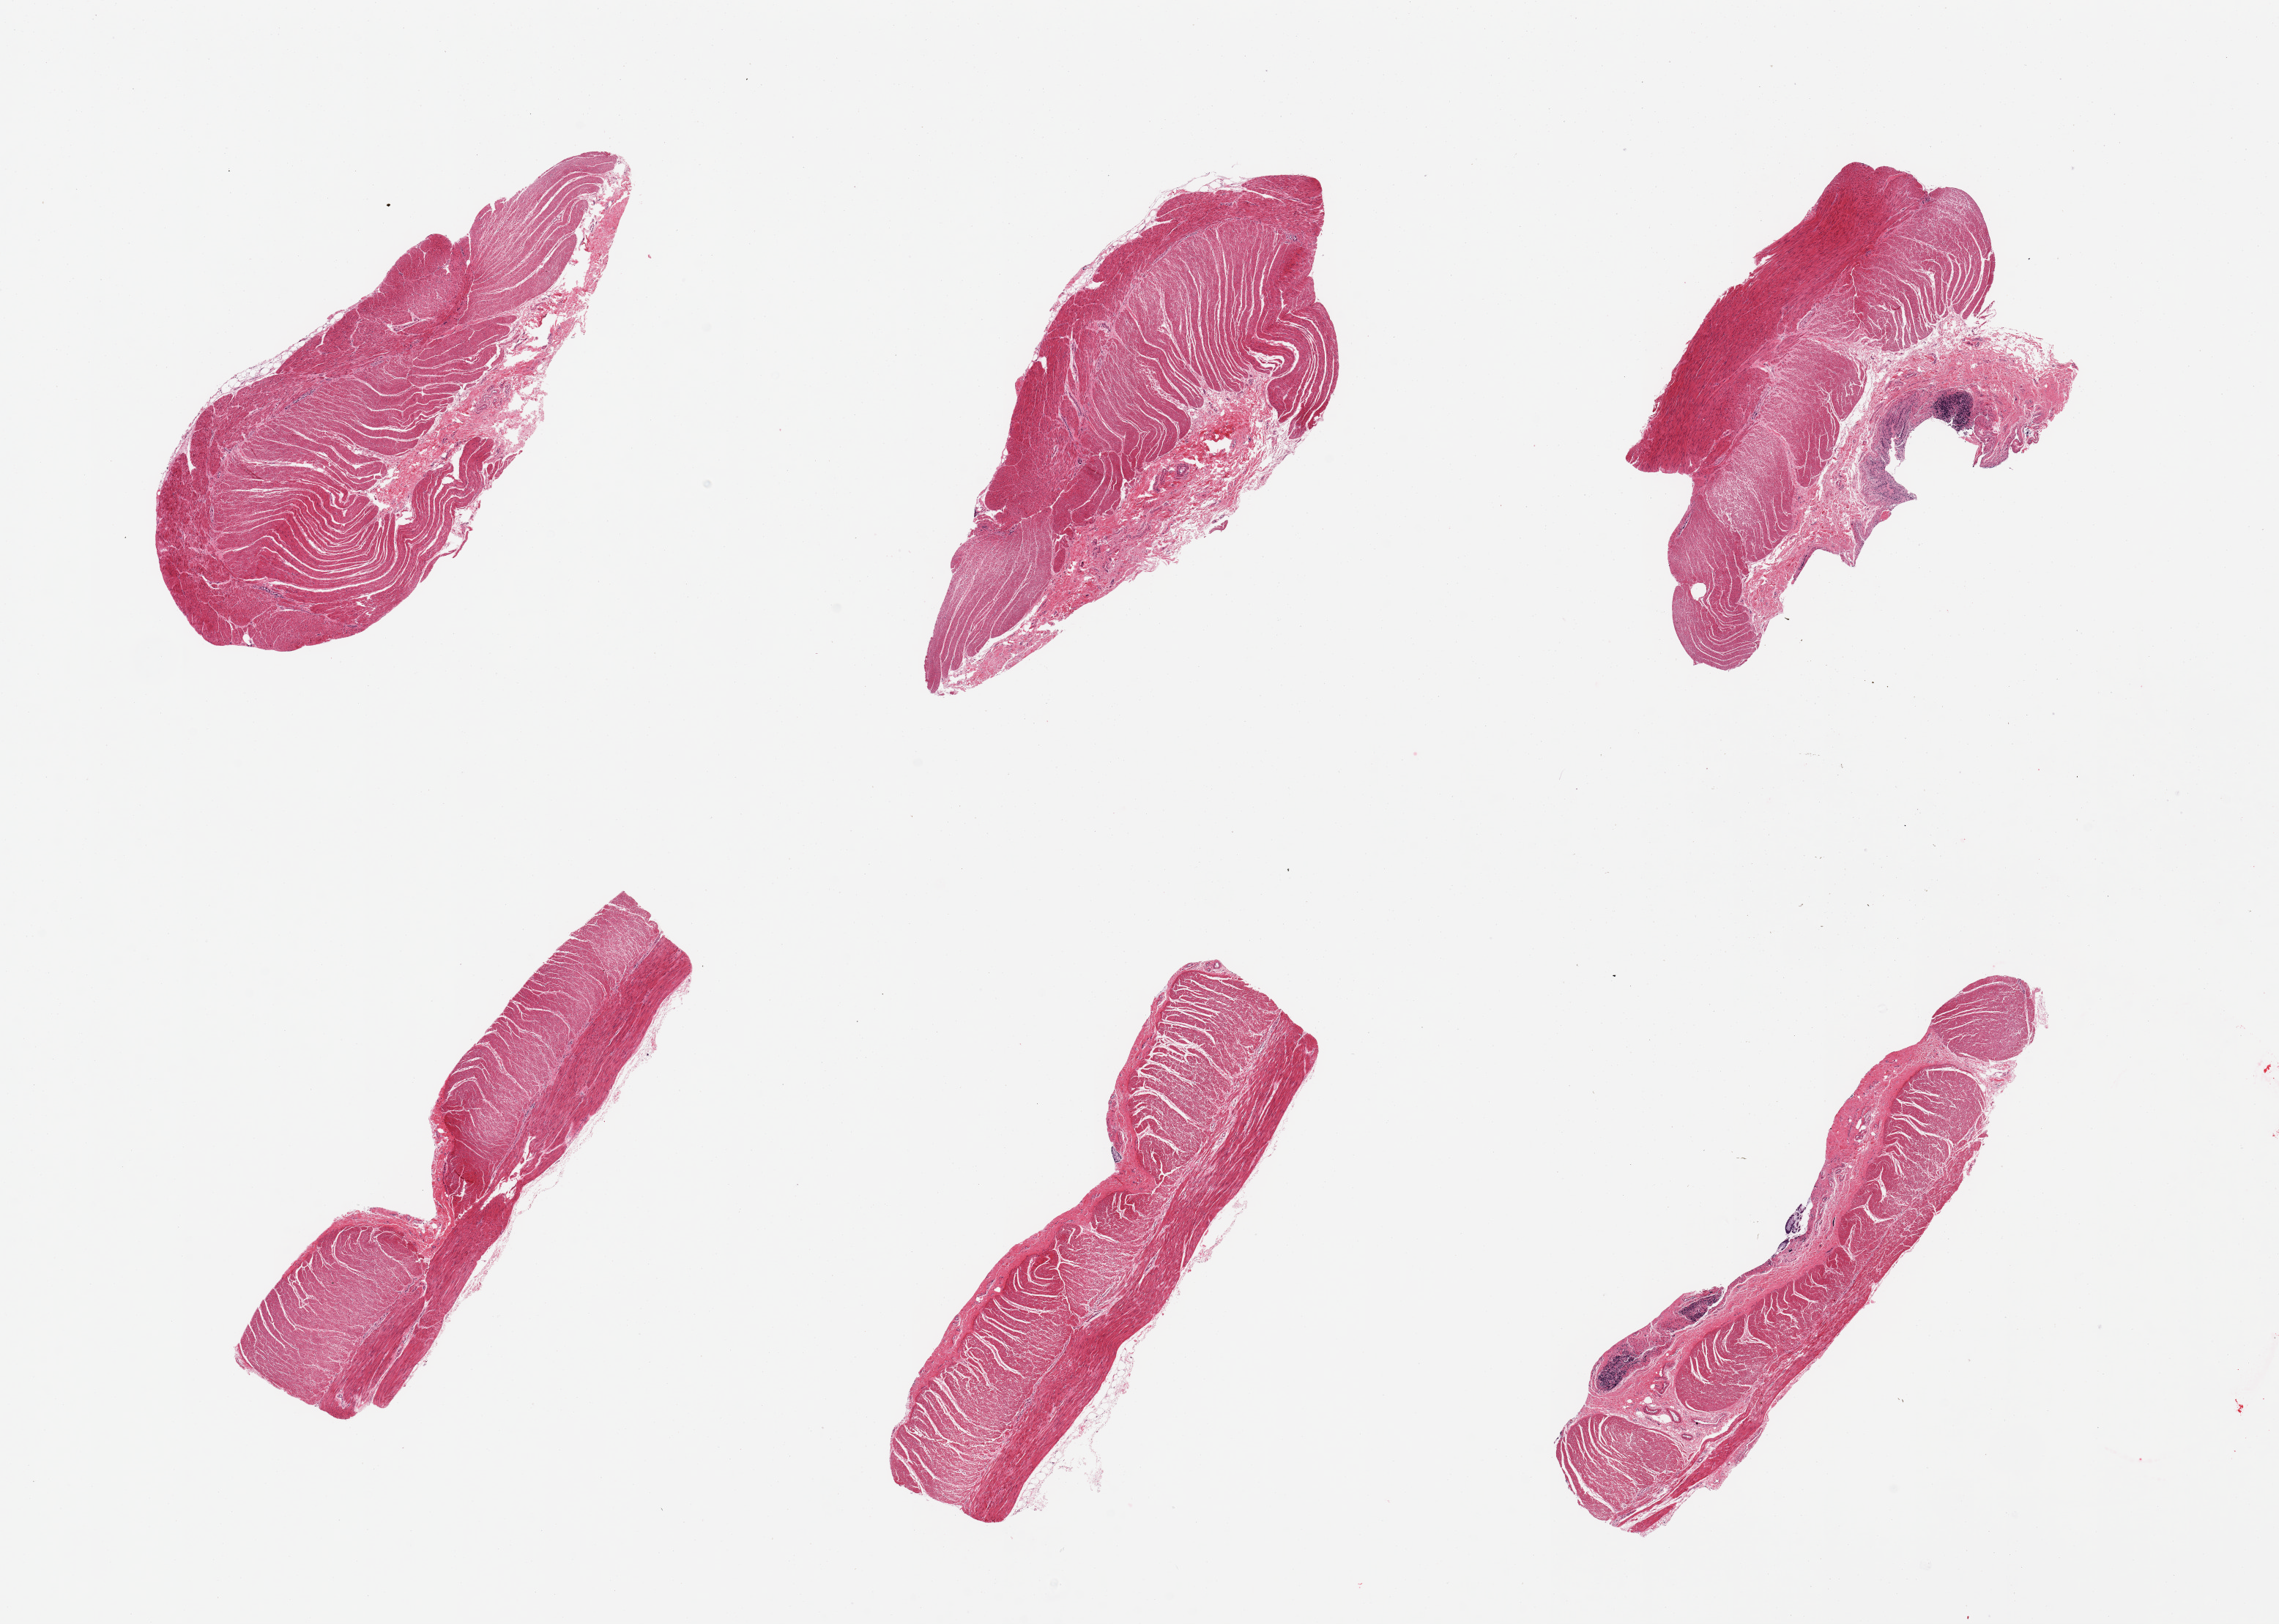
H&E whole-slide image, brightfield — whole scanned area (about 24.6 x 17.5 mm) shown as a low-resolution overview. PAXgene-fixed paraffin-embedded (PFPE) section. Target tissue: sigmoid colon. Donor tissue sample. Donor: female.
Reviewer comment on this tissue sample: 6 pieces; small foci of mucosa on 2.